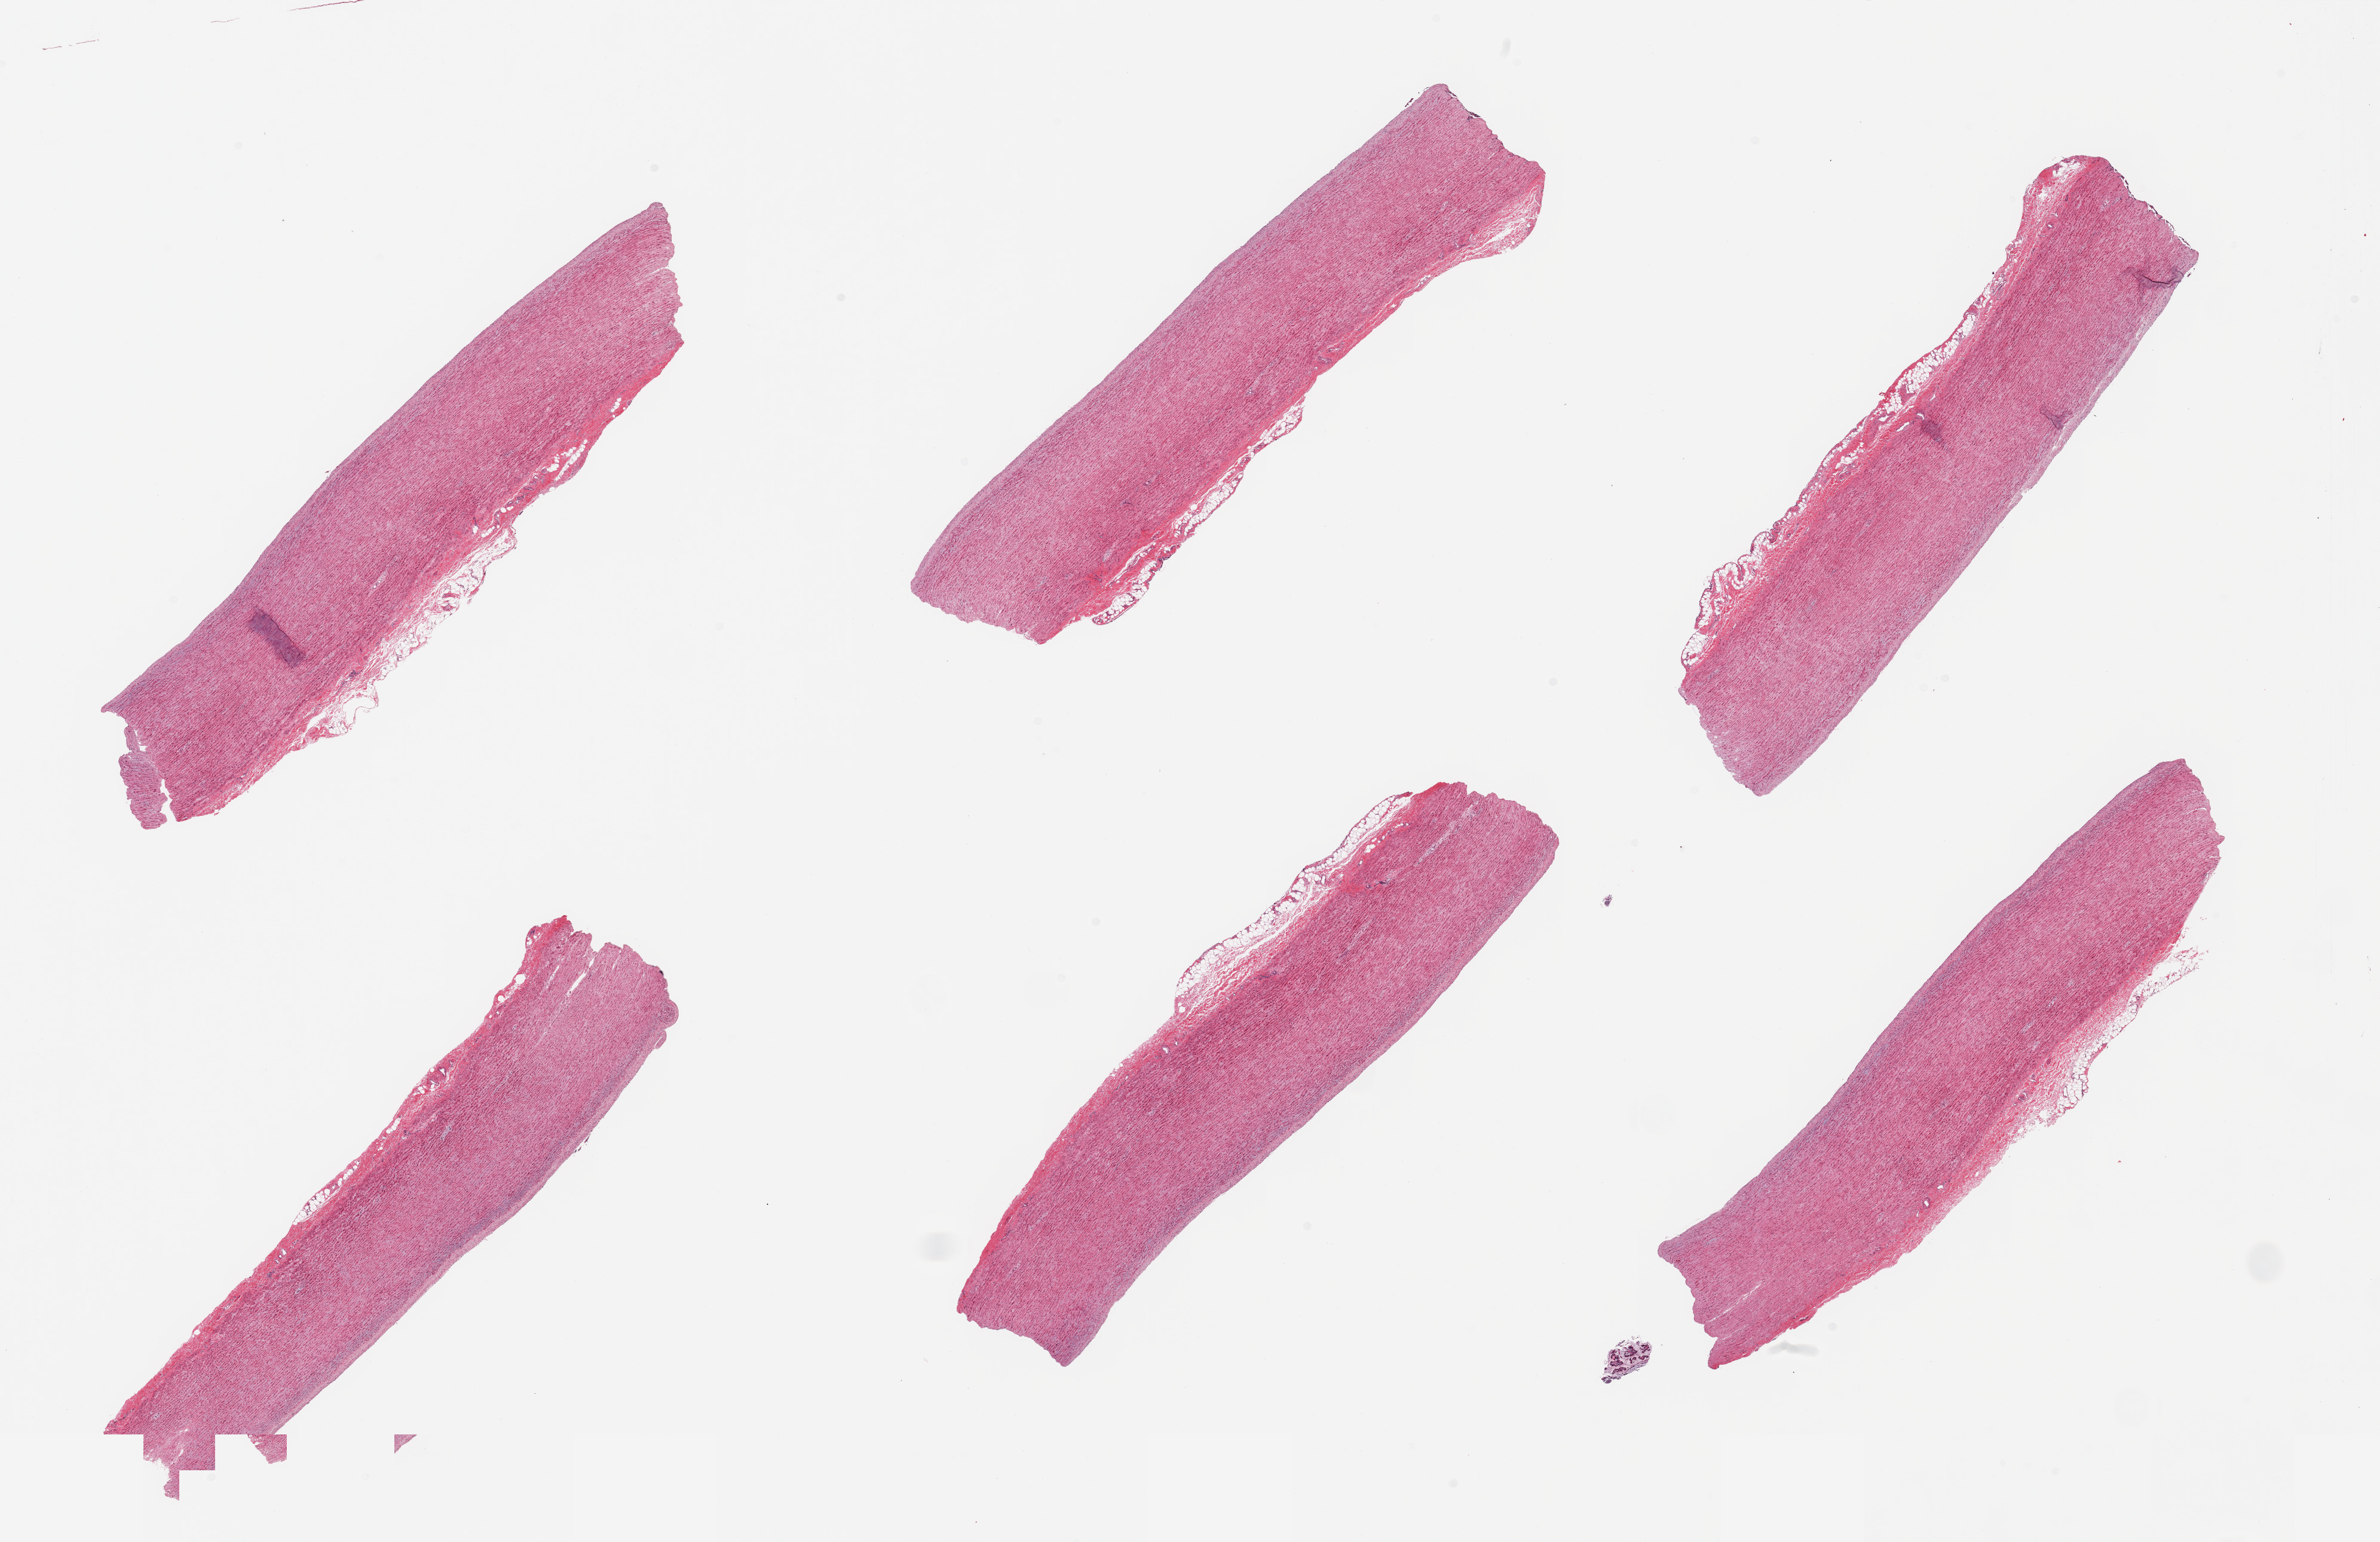
Digitized H&E-stained section, brightfield, whole scanned area (about 31.5 x 20.4 mm, from a 20x scan) shown as a low-resolution overview; PAXgene-fixed, paraffin-embedded tissue; target tissue: aorta; tissue donor sample. Donor: male.
- reviewer comment on this tissue sample: 6 pieces; no plaques; well dissected